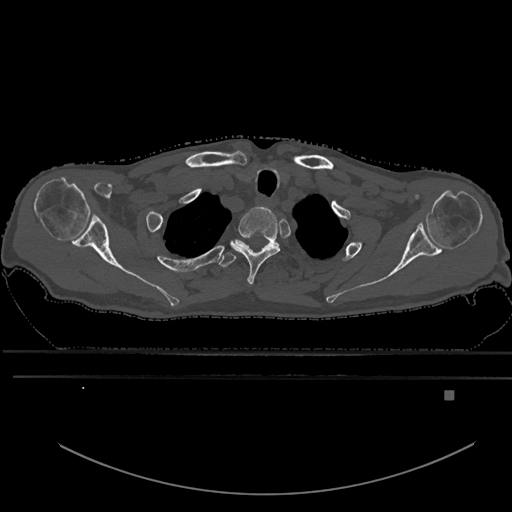
CT including the spine, one axial slice. Slice 526 of 969 in the series (ordered by position). Bone window (W 1800 / L 400 HU). 0.5 mm slice thickness. 512 × 512 image matrix, field of view 456 × 456 mm. Patient: male, 82 years. From the clinical record (not read from this slice): primary cancer: prostate; vertebrae with lytic lesions (as recorded): T11, T9, T8, T2.
Structures marked on this image (semi-automatically segmented with operator editing):
- T1 vertebra: bounding box <231,207,281,286> (left, top, right, bottom; pixels)
- T2 vertebra: <219,238,280,267>